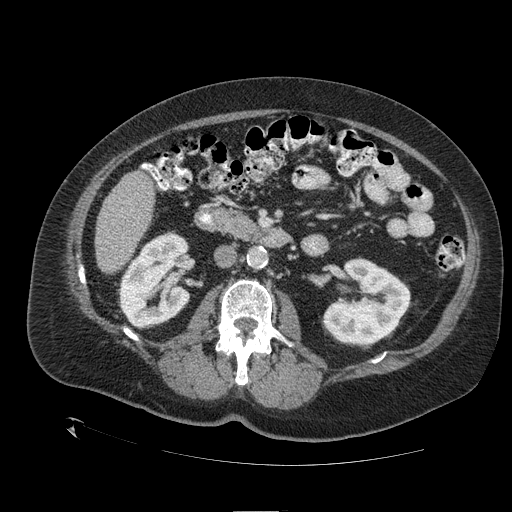
Contrast-enhanced abdominal CT (liver protocol), one axial slice; slice 41 of 109 in the series (ordered by position); reconstruction kernel STANDARD; one of 2 acquisitions stored at this slice position; soft-tissue window (W 400 / L 40 HU); 512 × 512 image matrix, field of view 460 × 460 mm. From the clinical record (not read from this slice): diagnosis: hepatocellular carcinoma (patient treated with transarterial chemoembolisation; whether this scan precedes or follows treatment is not stated here); TNM stage (as recorded): Stage-I; Child-Pugh class: A; tumour nodularity: uninodular.
Outlined on this slice (semi-automatic segmentation, software-assisted and operator-edited):
- liver parenchyma outside the tumour (the mass and vessels are separate outlines, so this box may not span the whole liver): bounding box (x1, y1, x2, y2) in pixels: (94, 170, 154, 274)